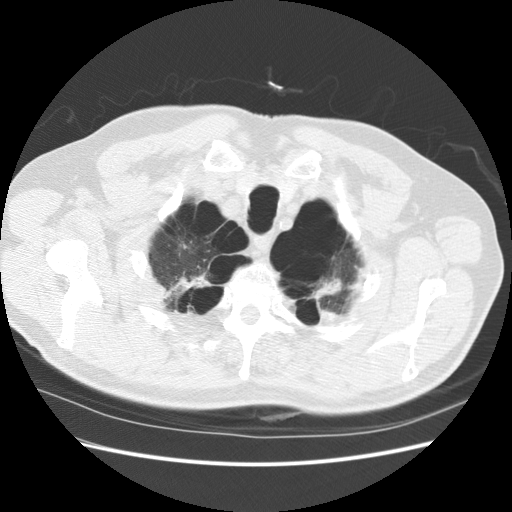
Axial slice from a low-dose chest CT screening exam, baseline screening round, lung window (W 1500 / L -600 HU), standard (soft-tissue) reconstruction kernel (STANDARD), slice 19 of 151 in the series, 512 × 512 image matrix, field of view 360 × 360 mm. Male participant, aged 68 years at enrolment.
• Expert reader's lesion annotation, bounding box (x1, y1, x2, y2) in pixels: (146, 260, 217, 325).
• The screening reader recorded 2 non-calcified nodules or masses ≥4 mm on this exam (left lower lobe, lingula); which of them this box marks is not recorded.
• Official screen result: positive, change unspecified: nodule(s) >= 4 mm or enlarging nodule(s), mass(es), or other non-specific abnormalities suspicious for lung cancer.
• Participant outcome: lung cancer diagnosed 1003 days after this screen (after the third annual screen) — large cell carcinoma, NOS, right upper lobe, poorly differentiated (G3), stage IV (AJCC 6th edition).